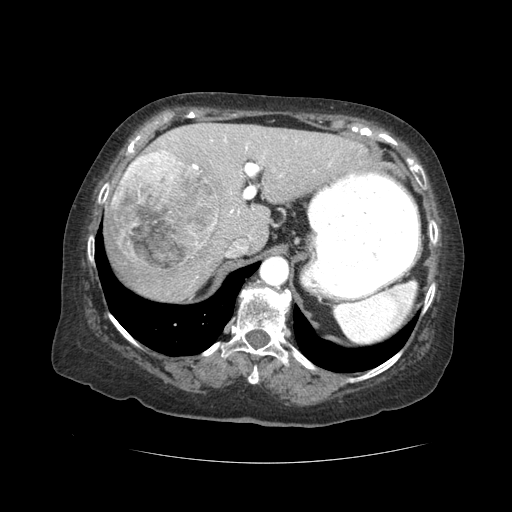
Contrast-enhanced abdominal CT (liver protocol), one axial slice; slice 30 of 59 in the series (ordered by position); reconstruction kernel STANDARD; soft-tissue window (W 400 / L 40 HU); 512 × 512 image matrix, field of view 380 × 380 mm. From the clinical record (not read from this slice): diagnosis: hepatocellular carcinoma (patient treated with transarterial chemoembolisation; whether this scan precedes or follows treatment is not stated here); TNM stage (as recorded): Stage-I; Child-Pugh class: A; tumour nodularity: uninodular.
Structures marked on this image (semi-automatically segmented with operator editing):
- abdominal aorta: bounding box (x1, y1, x2, y2) in pixels: (260, 257, 288, 286)
- liver parenchyma outside the tumour (the mass and vessels are separate outlines, so this box may not span the whole liver): (106, 123, 366, 300)
- mass: (112, 149, 218, 271)
- liver vessels: (192, 137, 331, 239)